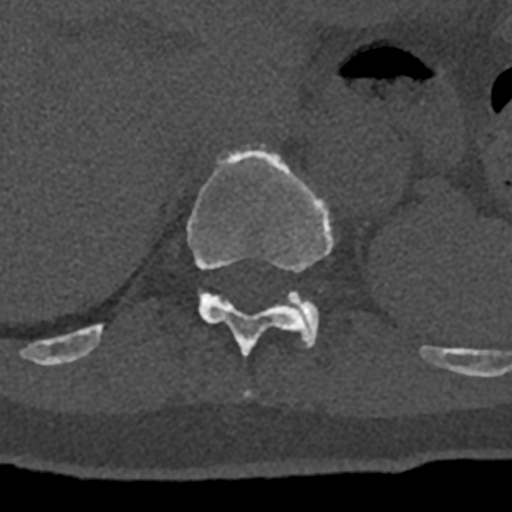
CT including the spine, one axial slice. Position 540 of 797 along the scan axis. Reconstruction kernel Br40s/3. 120 kVp. Bone window (W 1800 / L 400 HU). 512 × 512 image matrix, field of view 160 × 160 mm. Male patient, age 74 years. From the clinical record (not read from this slice): primary cancer: renal; vertebrae with lytic lesions (as recorded): T10, L1, L2, L3, L4, L5.
Structures marked on this image (semi-automatically segmented with operator editing):
- T10 vertebra: bounding box (x1, y1, x2, y2) in pixels: (243, 390, 250, 397)
- T11 vertebra: (70, 144, 432, 363)
- T12 vertebra: (287, 290, 319, 343)